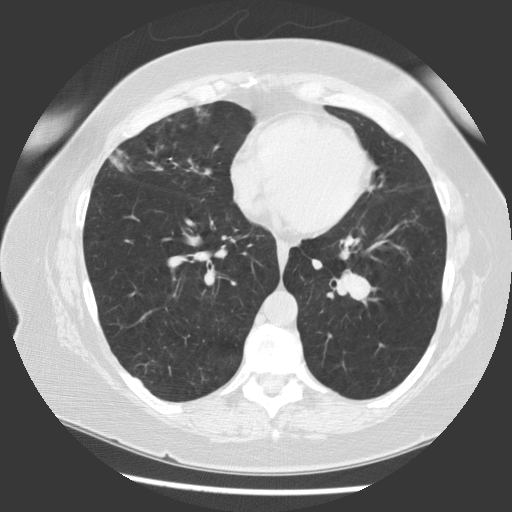
Axial slice from a low-dose chest CT screening exam, baseline screening round, lung window (W 1500 / L -600 HU), standard (soft-tissue) reconstruction kernel (STANDARD), slice 55 of 130 in the series, 512 × 512 image matrix. Female, age 58 years at enrolment.
- Expert reader's lesion annotation, bounding box <328,259,390,324> (left, top, right, bottom; pixels).
- Reader record for this screening exam (exam-level; its link to the box is not recorded): non-calcified nodule or mass ≥4 mm, left lower lobe, 22 × 15 mm, smooth margins, soft tissue attenuation.
- Participant outcome: lung cancer diagnosed 108 days after this screen — carcinoma, NOS, left hilum, stage IA (AJCC 6th edition), 28 mm at pathology.